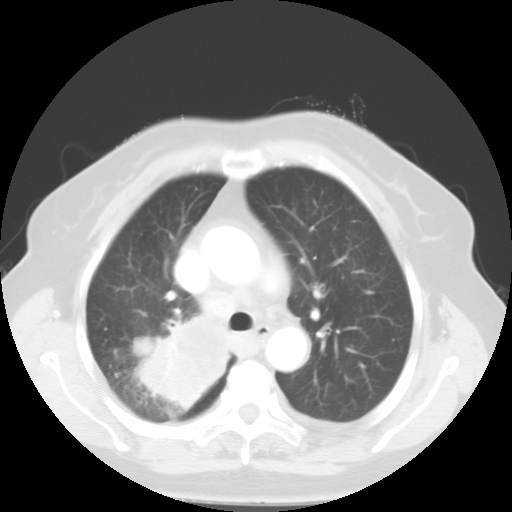
Chest CT, one axial slice; position 37 of 52 along the scan axis; reconstruction kernel STANDARD; lung window (W 1500 / L -600 HU); 5 mm slice thickness; 512 × 512 image matrix, field of view 333 × 333 mm. Female patient, age 81 years. From the clinical record (not read from this slice): clinical TNM (as recorded): T4 N3 M1b.
Outlined on this slice (rectangle marked by the reading radiologist):
- lung tumour (recorded histology: adenocarcinoma): bounding box [x1, y1, x2, y2] px = [133, 310, 232, 408]